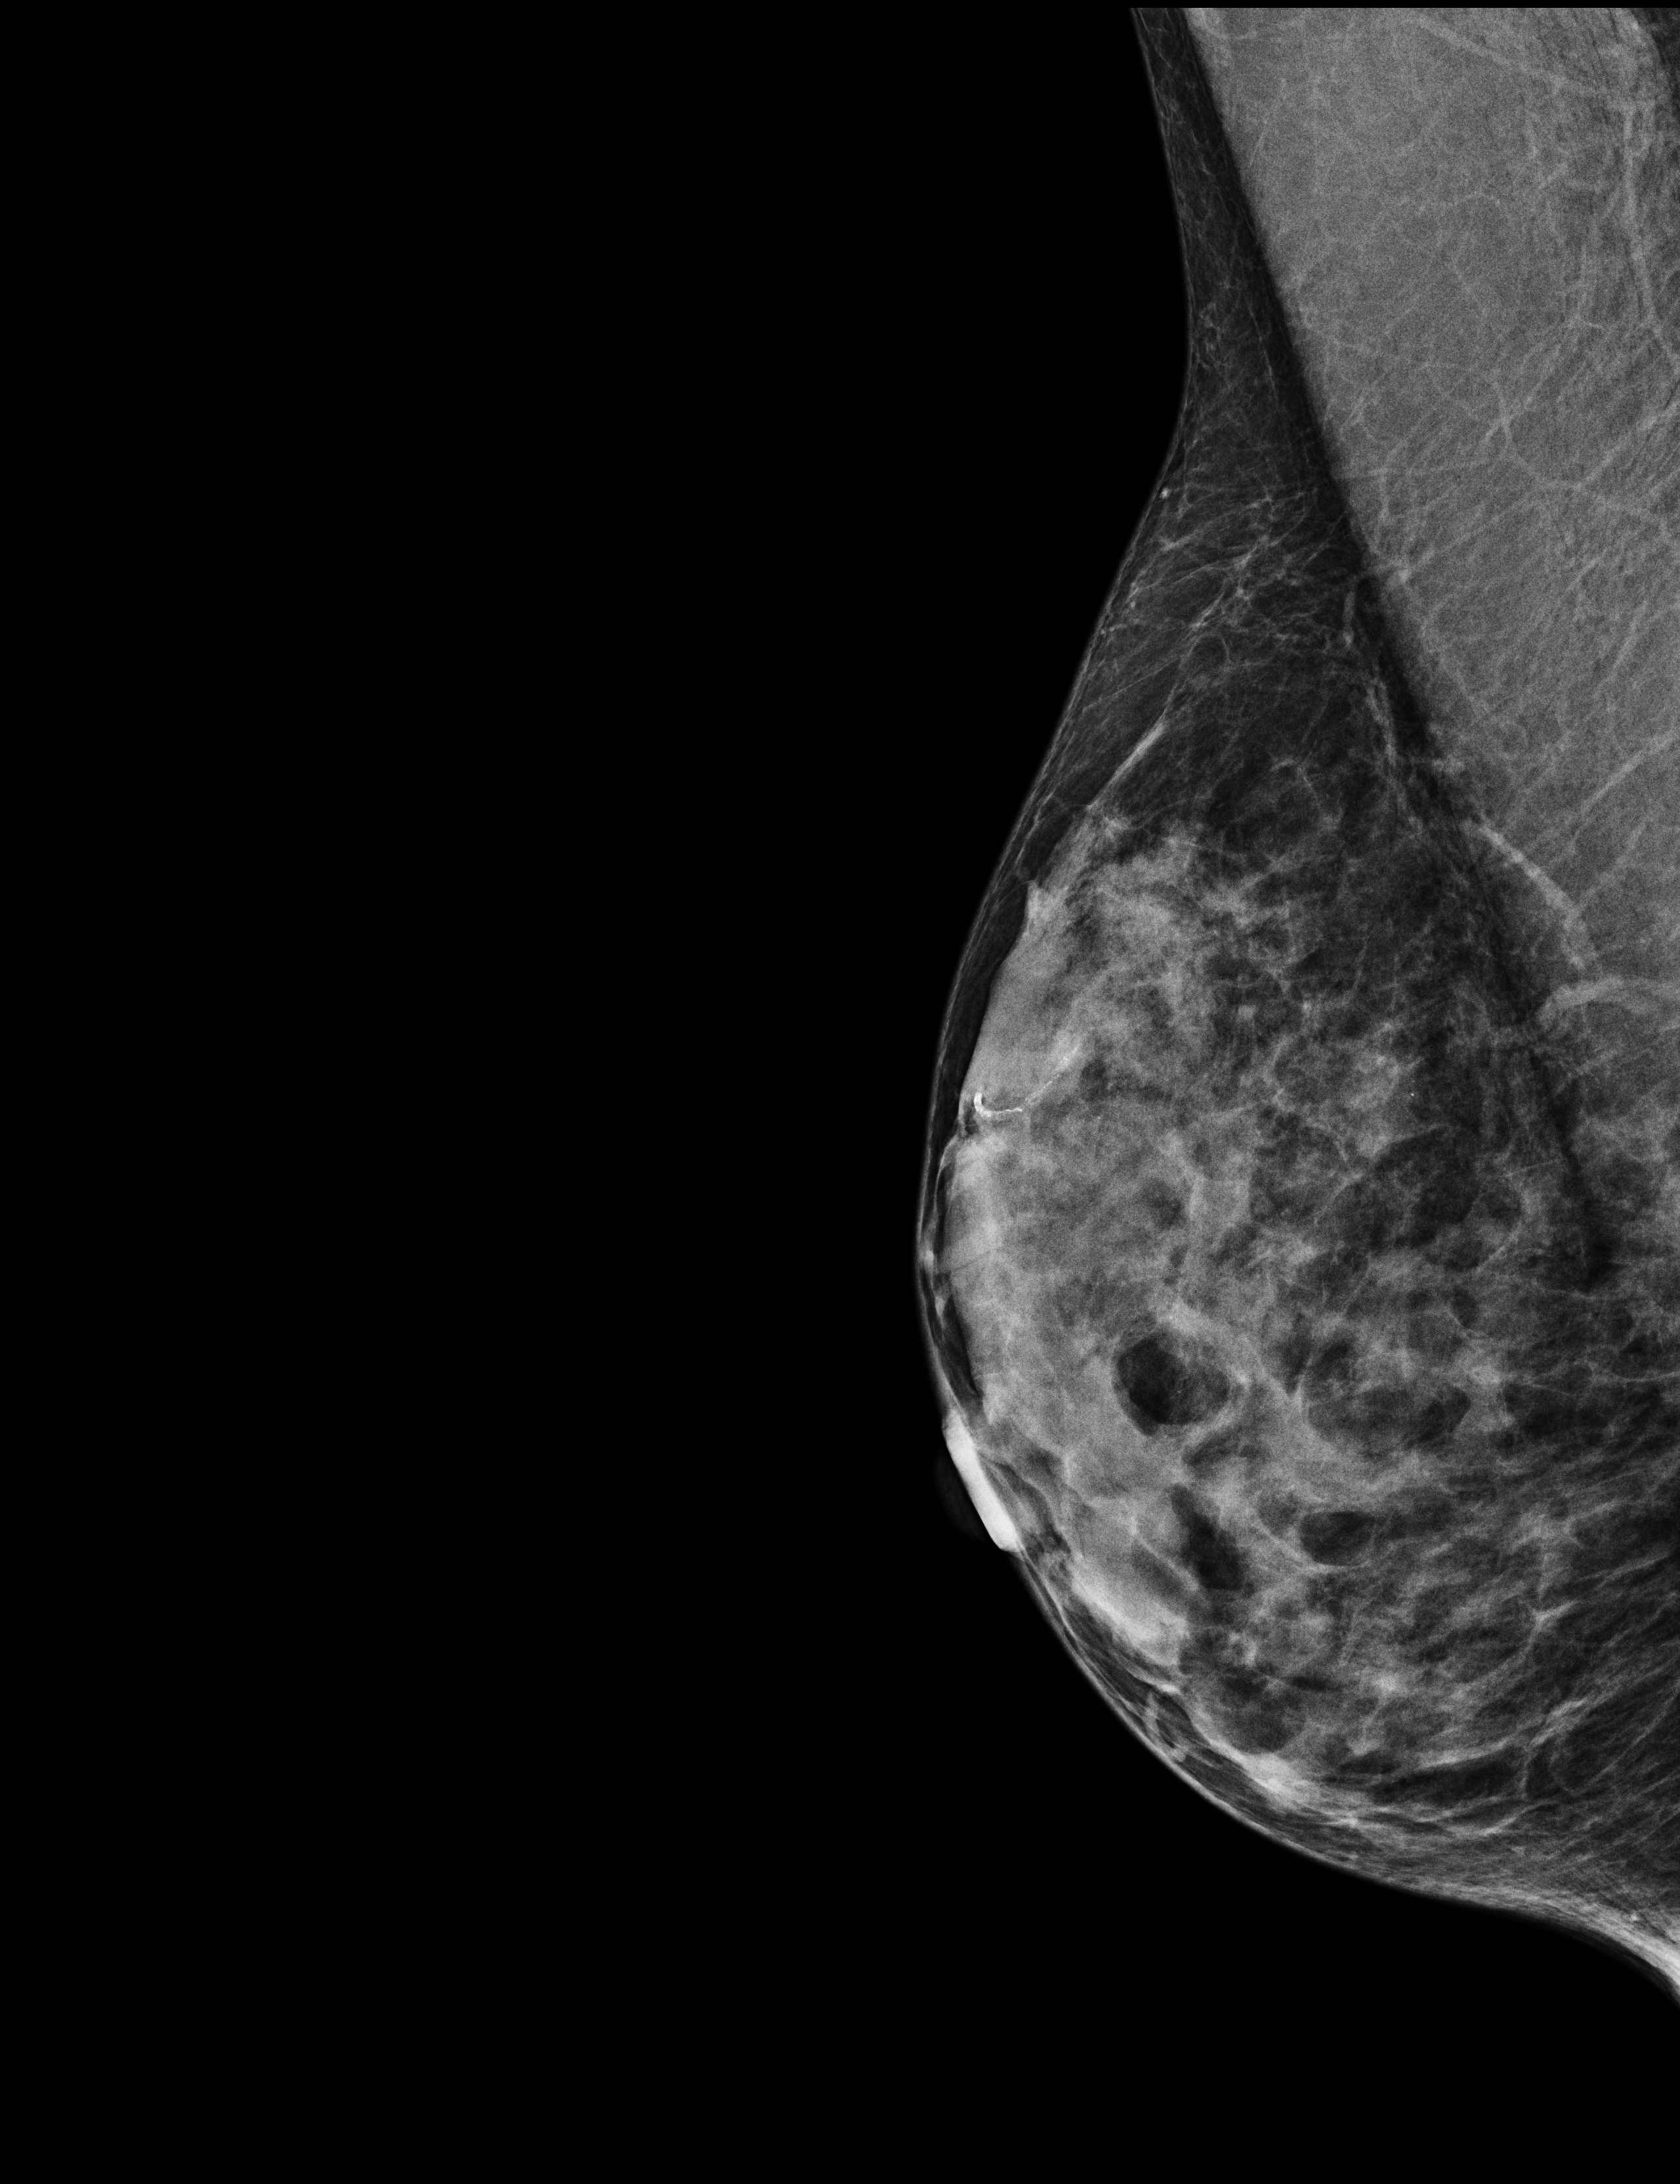
Screening examination. Female patient, age 59 years.
Image type: full-field digital mammogram. Breast: right. Projection: MLO view.